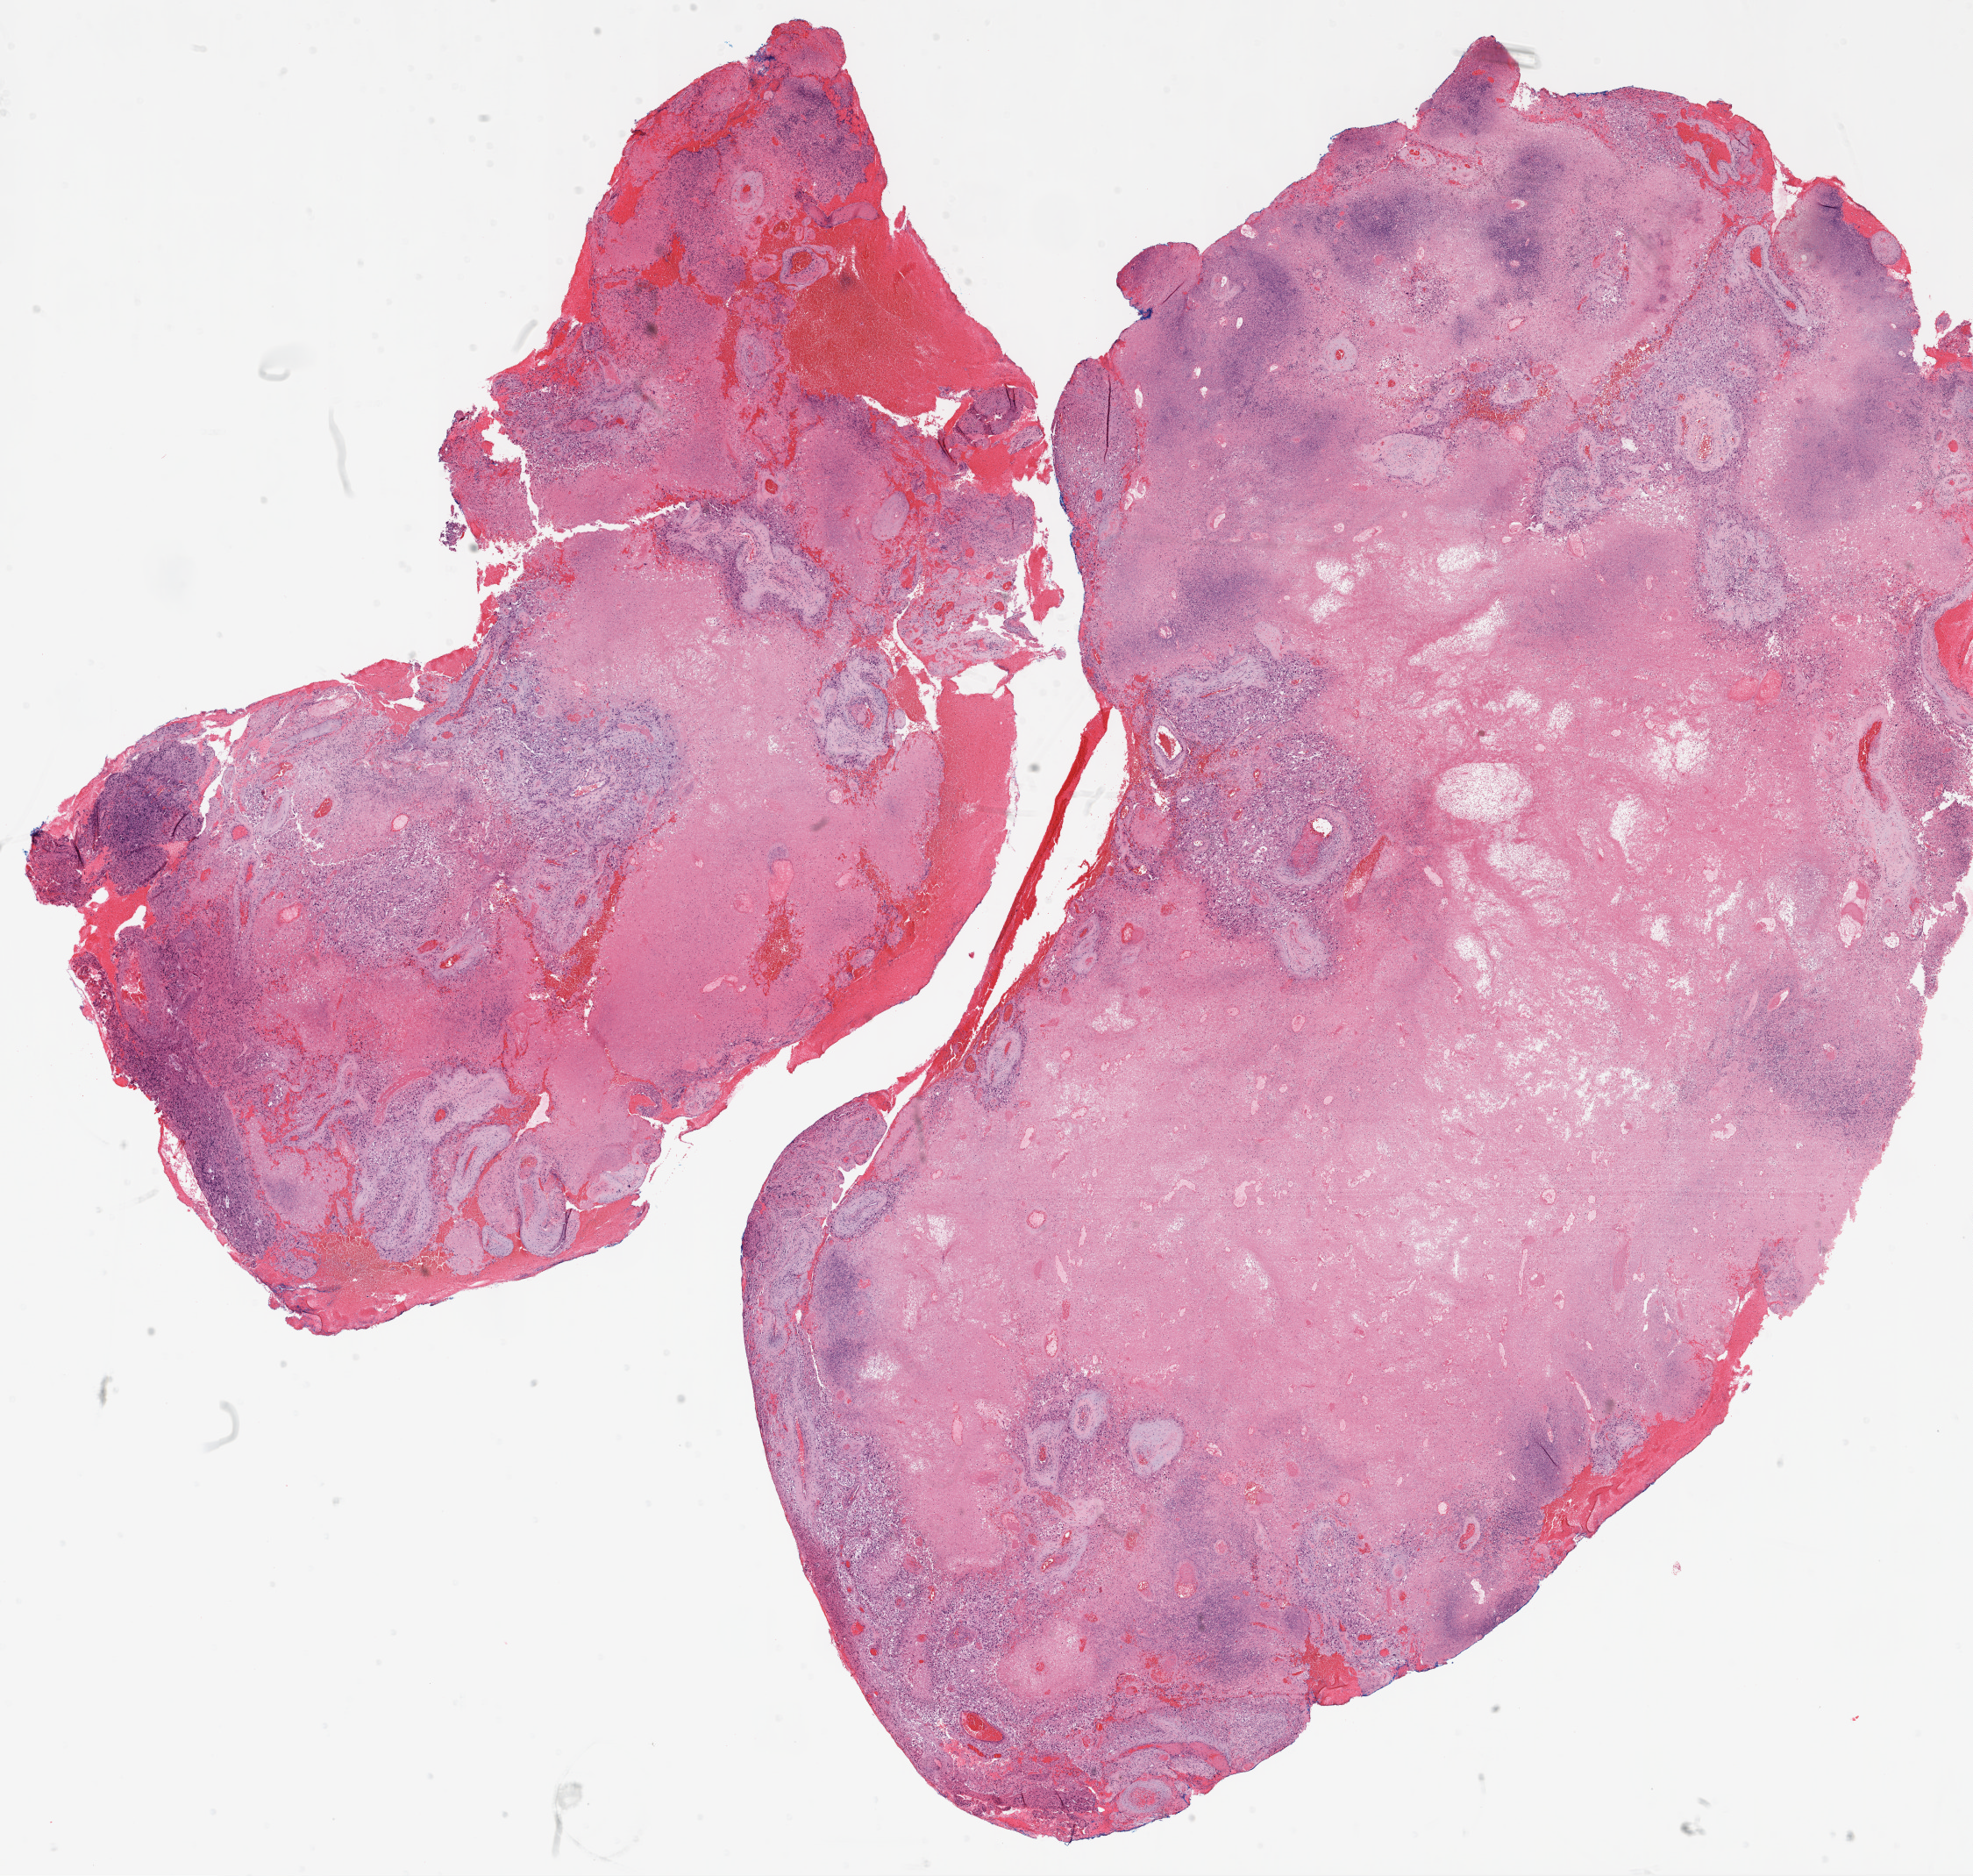
Whole-slide histology image, H&E, whole scanned area (about 18.1 x 17.2 mm, acquisition: 20x scan) shown as a low-resolution overview; formalin-fixed paraffin-embedded (FFPE) diagnostic section; primary tumour sample from the brain. Patient: male, age at initial diagnosis 66 years.
Diagnosis: Glioblastoma.